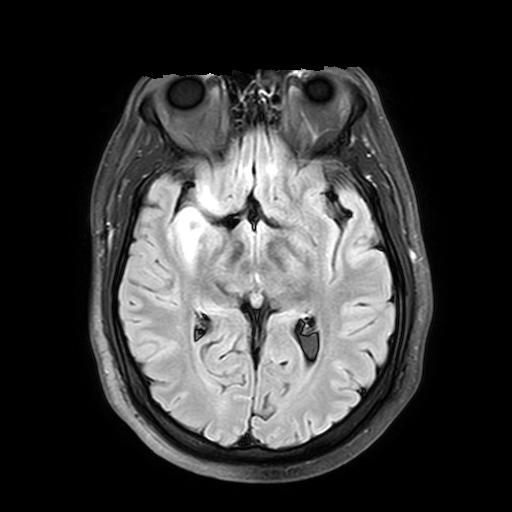
Brain MRI from a brain-tumour surgery series, one axial slice. Position 23 of 42 along the scan axis. T2 FLAIR. 4 mm slice thickness. 512 × 512 image matrix, field of view 240 × 240 mm. Case-level facts recorded for this patient, not image findings: histopathology: Astrocytoma; WHO grade: 2; IDH mutation: yes; tumour location: Right Insular.
Structures marked on this image (manually delineated by an expert):
- tumour: box from (x=137, y=205) to (x=223, y=260) px